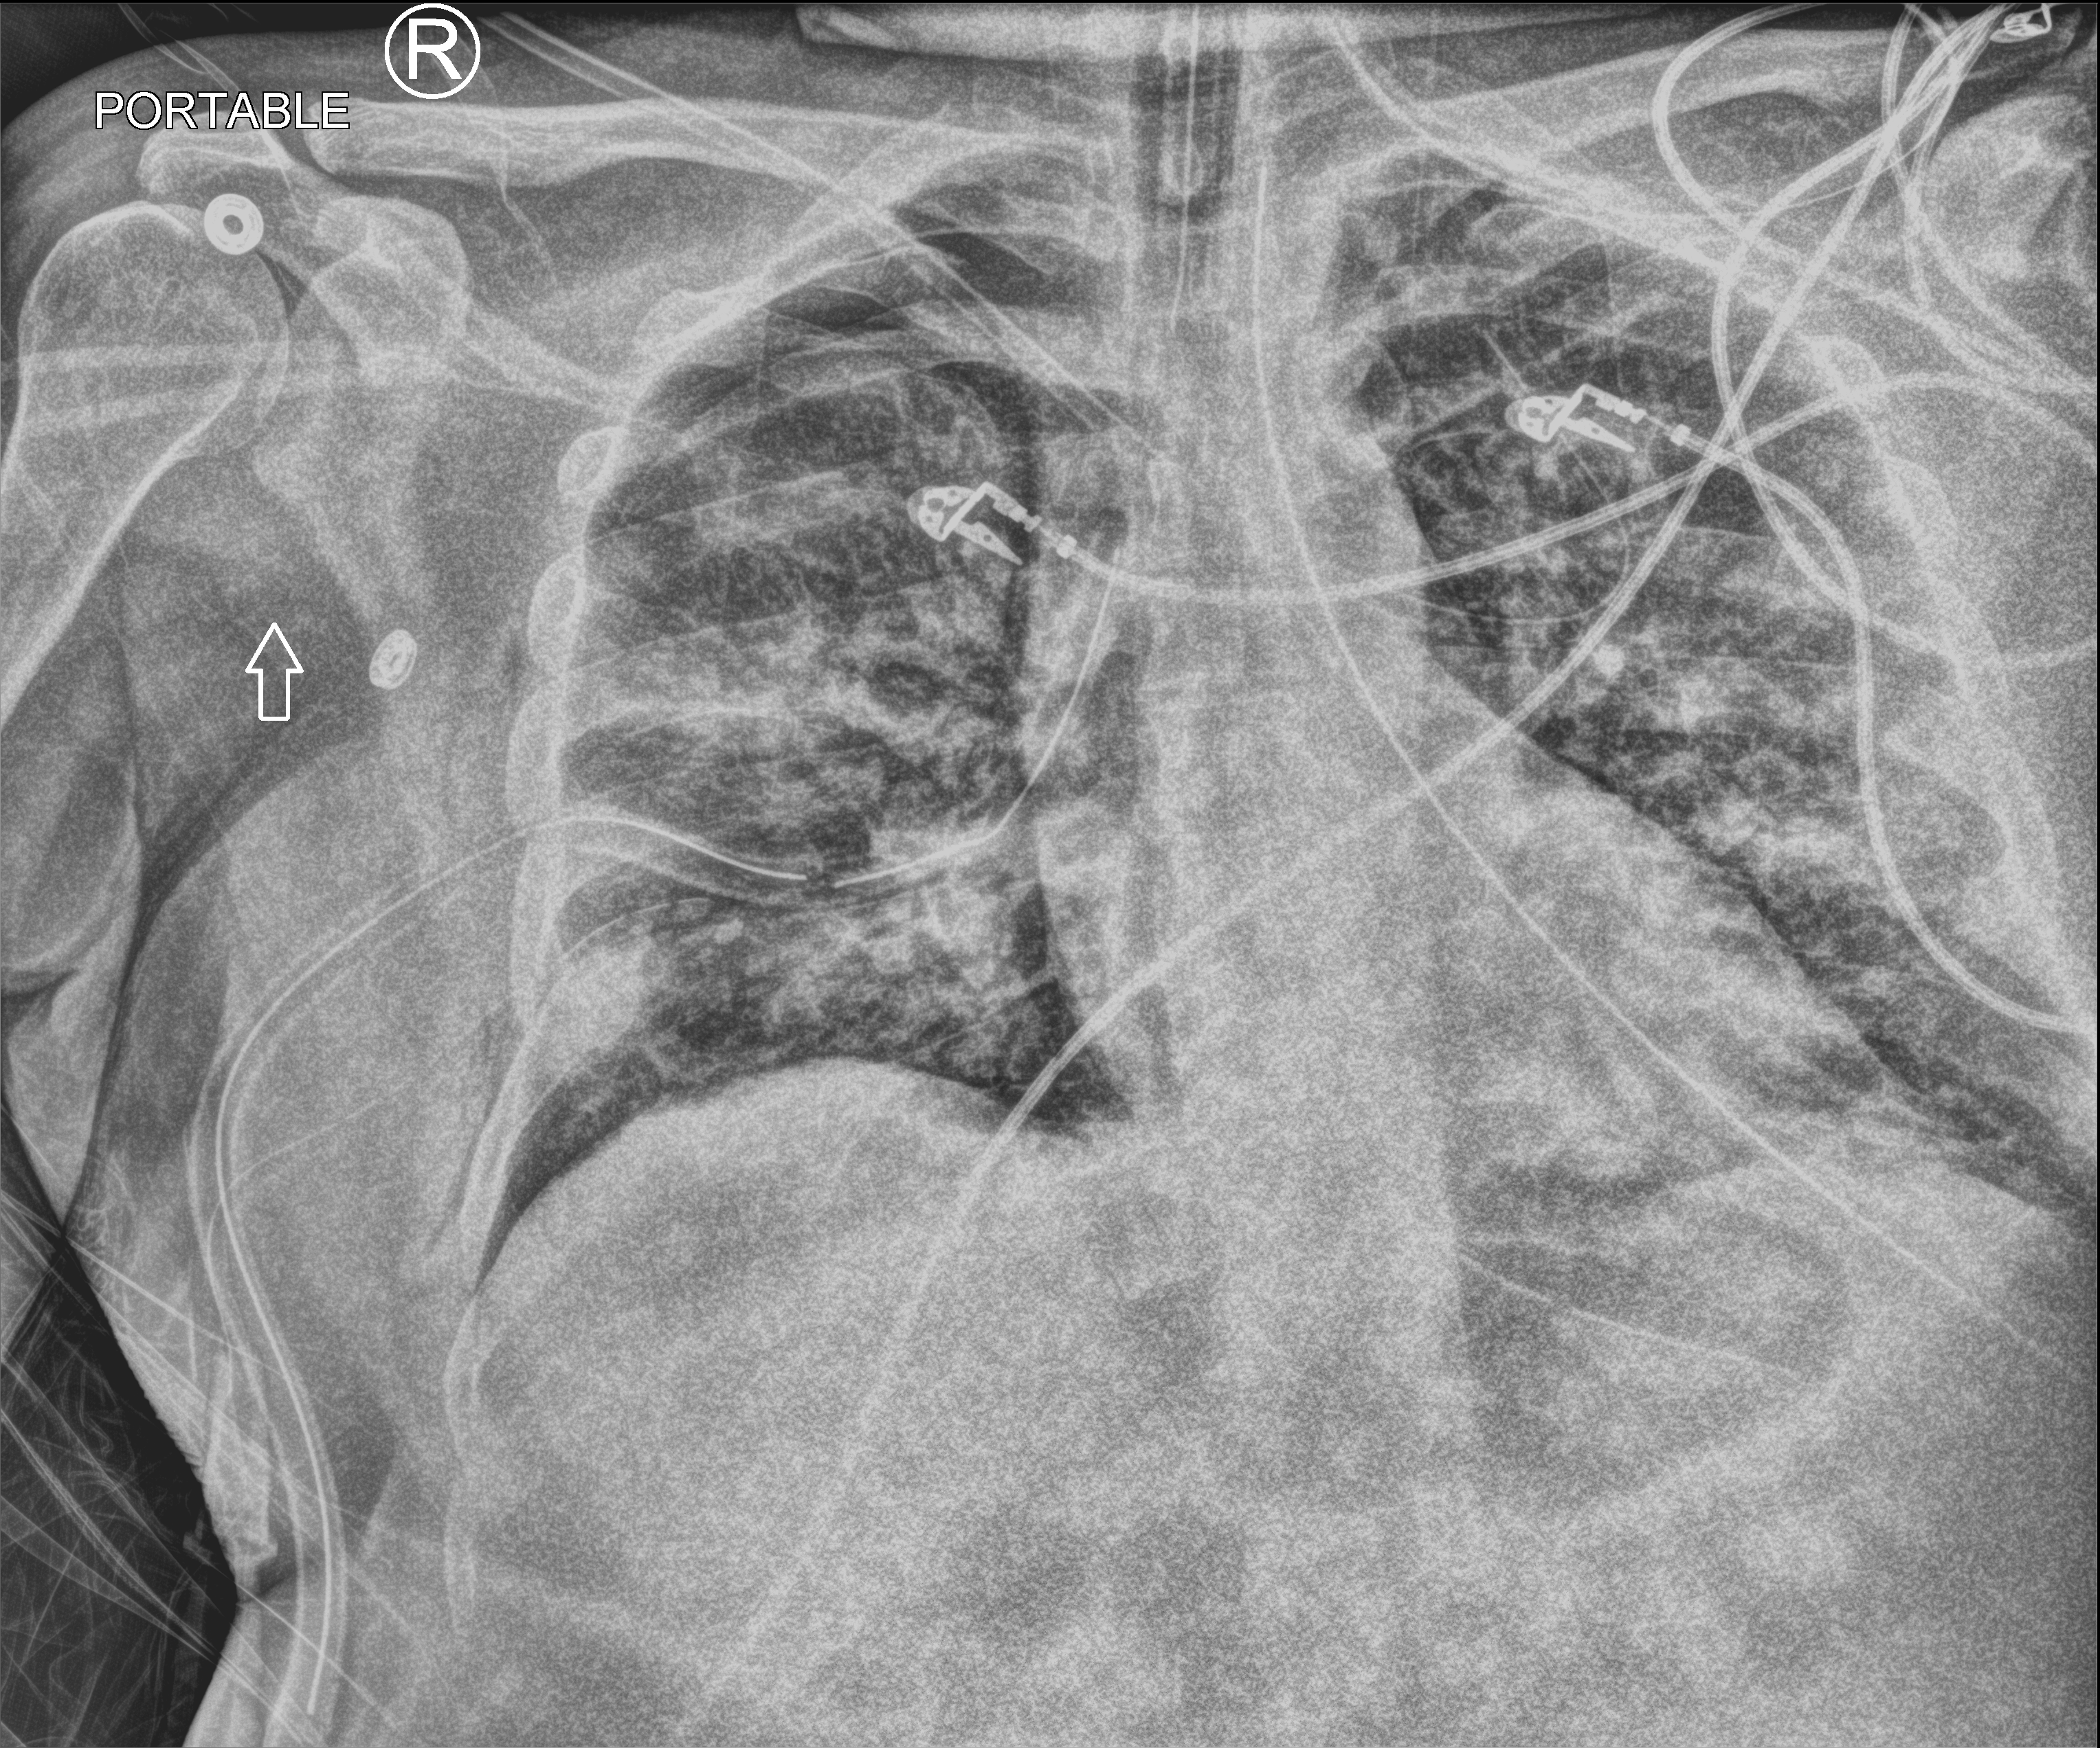
Portable chest radiograph; anteroposterior (AP) projection. Male patient hospitalised with COVID-19, age 18–59 years.
Admission-level facts for this patient (not findings on this image; timing relative to this image not recorded): chronic kidney disease (admission record): no; smoking status (admission record): never.